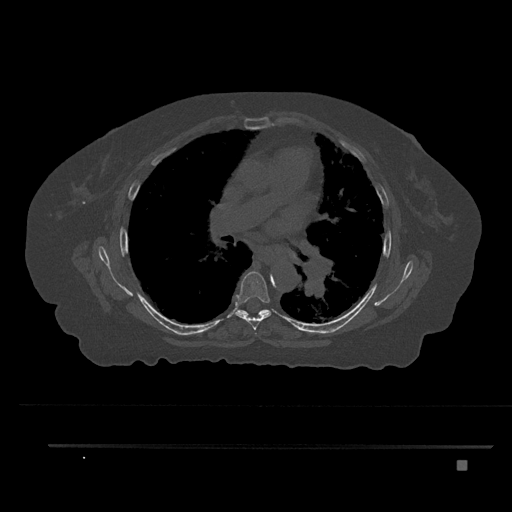
CT including the spine, one axial slice. Slice 518 of 797 in the series (ordered by position). Reconstruction kernel Br40s/3. 120 kVp. Bone window (W 1800 / L 400 HU). 512 × 512 image matrix. Female patient, age 76 years. Case-level facts recorded for this patient, not image findings: primary cancer: lung; vertebrae with lytic lesions (as recorded): T11, L3.
Outlined on this slice (semi-automatically segmented with operator editing):
- T6 vertebra: bounding box (x1, y1, x2, y2) in pixels: (235, 271, 271, 330)
- T7 vertebra: (237, 309, 269, 318)